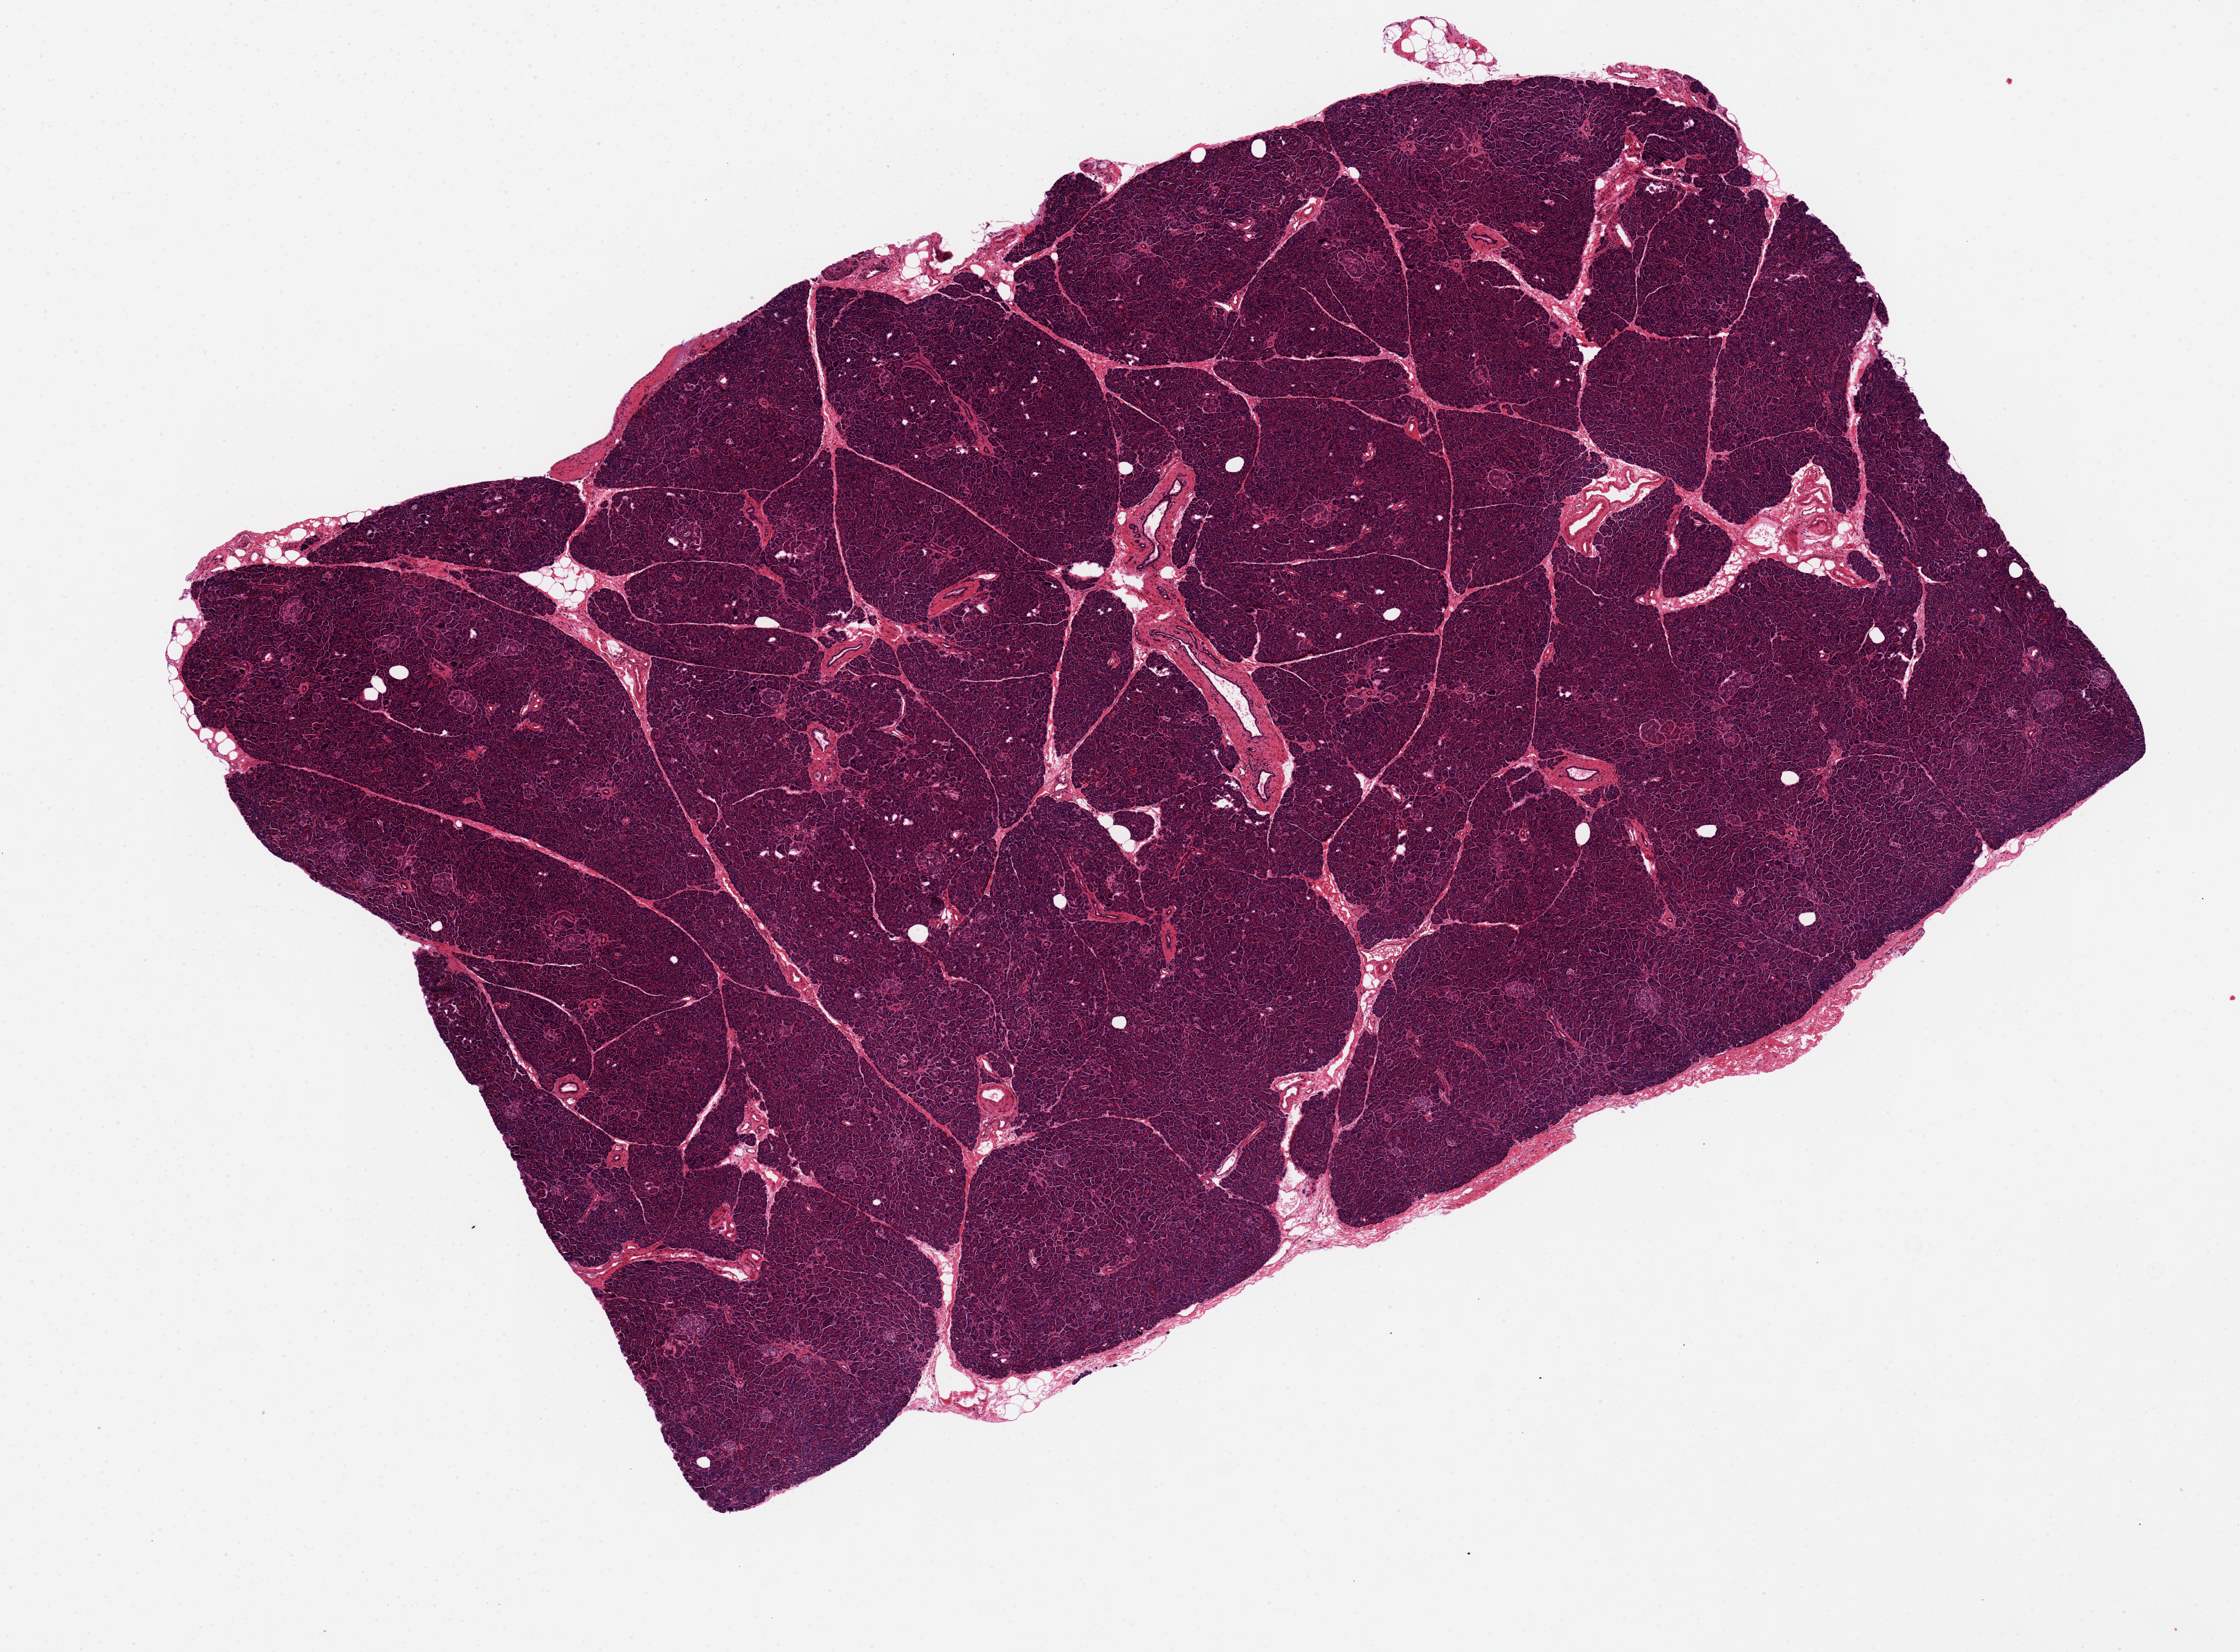
H&E whole-slide image — shown as a low-resolution overview of the whole scanned area (about 12.8 x 9.4 mm, from a 20x scan), PAXgene-fixed, paraffin-embedded tissue, section of pancreas (target tissue), donor tissue sample. Donor: female.
- pathologist's review note for this sample: Well preserved, minimal fat. 9 x 6 mm